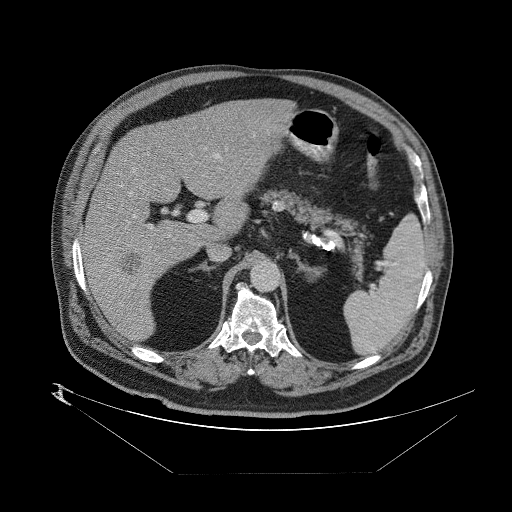
Contrast-enhanced abdominal CT (liver protocol), one axial slice; slice 45 of 89 in the series (ordered by position); 140 kVp; one of 2 acquisitions stored at this slice position; soft-tissue window (W 400 / L 40 HU); 2.5 mm slice thickness; 512 × 512 image matrix. Case-level facts recorded for this patient, not image findings: diagnosis: hepatocellular carcinoma (patient treated with transarterial chemoembolisation; whether this scan precedes or follows treatment is not stated here); TNM stage (as recorded): Stage-II.
Structures marked on this image (semi-automatic segmentation, software-assisted and operator-edited):
- abdominal aorta: bounding box (x1, y1, x2, y2) in pixels: (252, 262, 279, 290)
- liver parenchyma outside the tumour (the mass and vessels are separate outlines, so this box may not span the whole liver): (82, 96, 282, 340)
- mass: (116, 247, 148, 274)
- liver vessels: (84, 127, 272, 311)